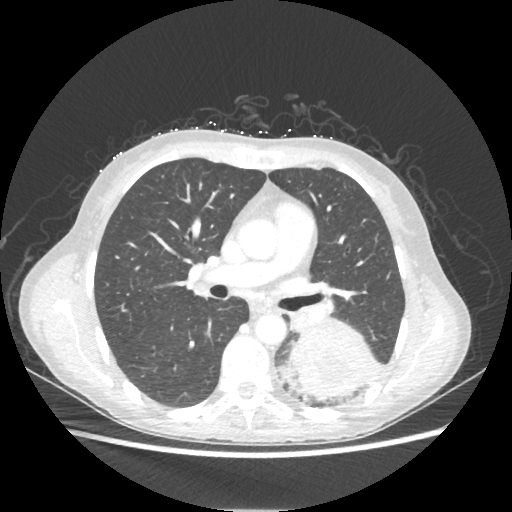
Chest CT, one axial slice. Position 122 of 221 along the scan axis. 80 kVp. Lung window (W 1500 / L -600 HU). 512 × 512 image matrix, field of view 360 × 360 mm. Patient: female, 53 years. Case-level facts recorded for this patient, not image findings: clinical TNM (as recorded): T3 N0 M0.
Outlined on this slice (rectangle marked by the reading radiologist):
- lung tumour (recorded histology: adenocarcinoma): bounding box [x1, y1, x2, y2] px = [290, 317, 377, 400]